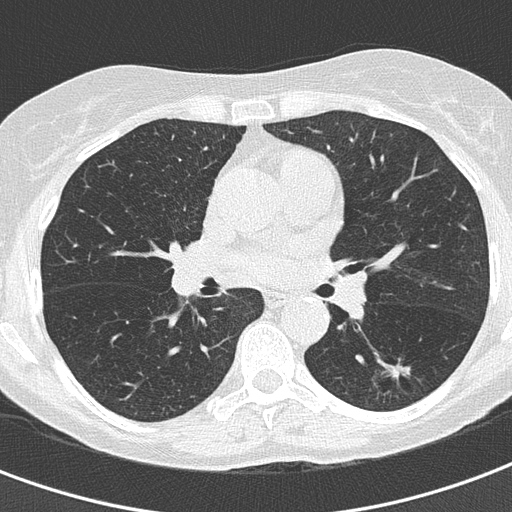
Axial slice from a low-dose chest CT screening exam. Second annual screen. Lung window (W 1500 / L -600 HU). Lung (sharp) reconstruction kernel (B50f). 512 × 512 image matrix, field of view 282 × 282 mm. Female participant, aged 60 years at enrolment.
- Lesion marked by an expert reader, box from (x=377, y=352) to (x=417, y=384) px.
- Screening reader's record for this exam (one nodule recorded; not confirmed to be the boxed lesion): non-calcified nodule or mass ≥4 mm, left lower lobe, 10 × 9 mm, soft tissue attenuation.
- Official screen result: positive, other.
- Later outcome: lung cancer diagnosed 64 days after this screen — adenocarcinoma, NOS, left lower lobe, well differentiated (G1), stage IA (AJCC 6th edition), 15 mm at pathology.